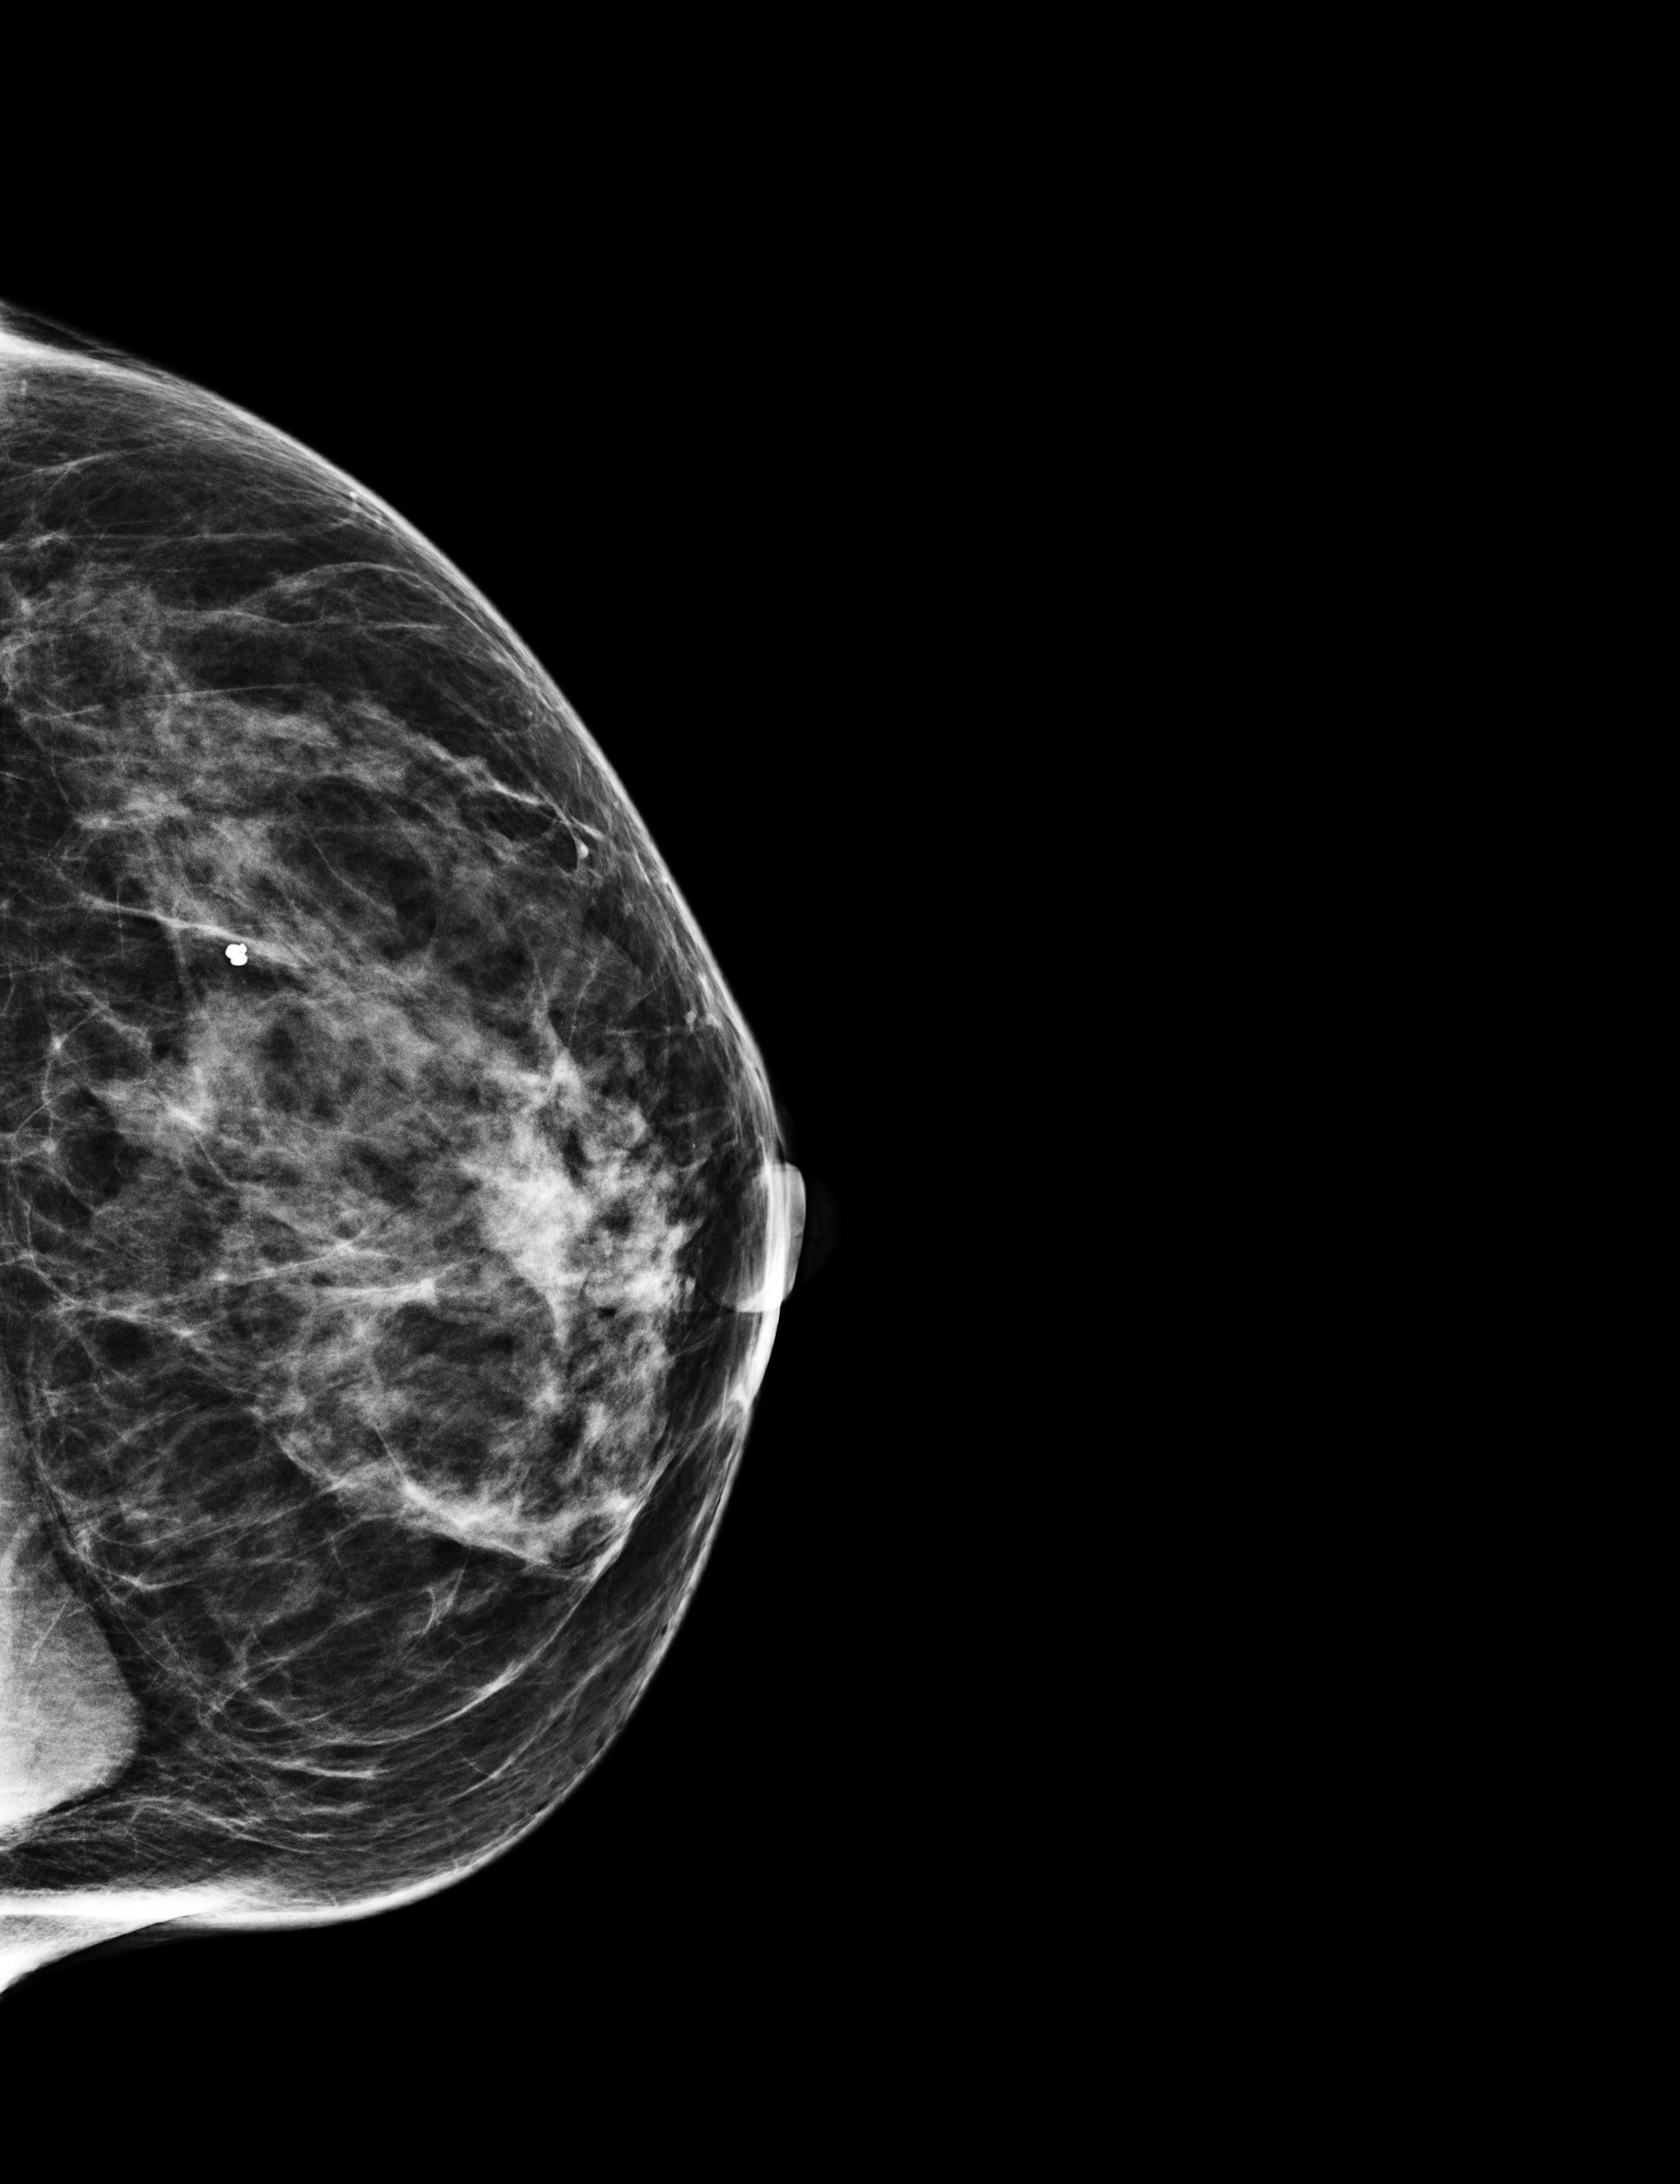
Digital mammogram (FFDM), left breast, craniocaudal (CC) view, annual screening mammography examination, system: Selenia Dimensions. Patient: female, 60 years.
BI-RADS breast density category at the screening exam (both breasts, scale 1–4): 3. Final BI-RADS category for the screening round (tomosynthesis exam, both breasts): category 1. Recall: recalled for additional imaging after this screen.